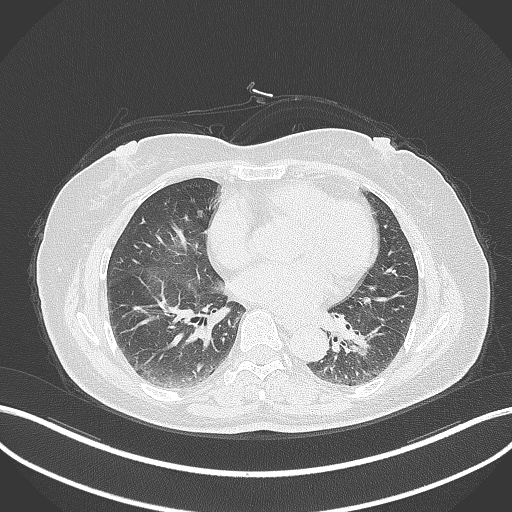
Chest CT, one axial slice; slice 164 of 311 in the series (ordered by position); reconstruction kernel B70f; 120 kVp; lung window (W 1500 / L -600 HU); 1 mm slice thickness; 512 × 512 image matrix, field of view 400 × 400 mm. Female patient, age 59 years. Case-level facts recorded for this patient, not image findings: clinical TNM (as recorded): T2a N0 M0; histopathological grade: G2-3.
Structures marked on this image (rectangle marked by the reading radiologist):
- lung tumour (recorded histology: adenocarcinoma): bounding box <343,326,383,360> (left, top, right, bottom; pixels)